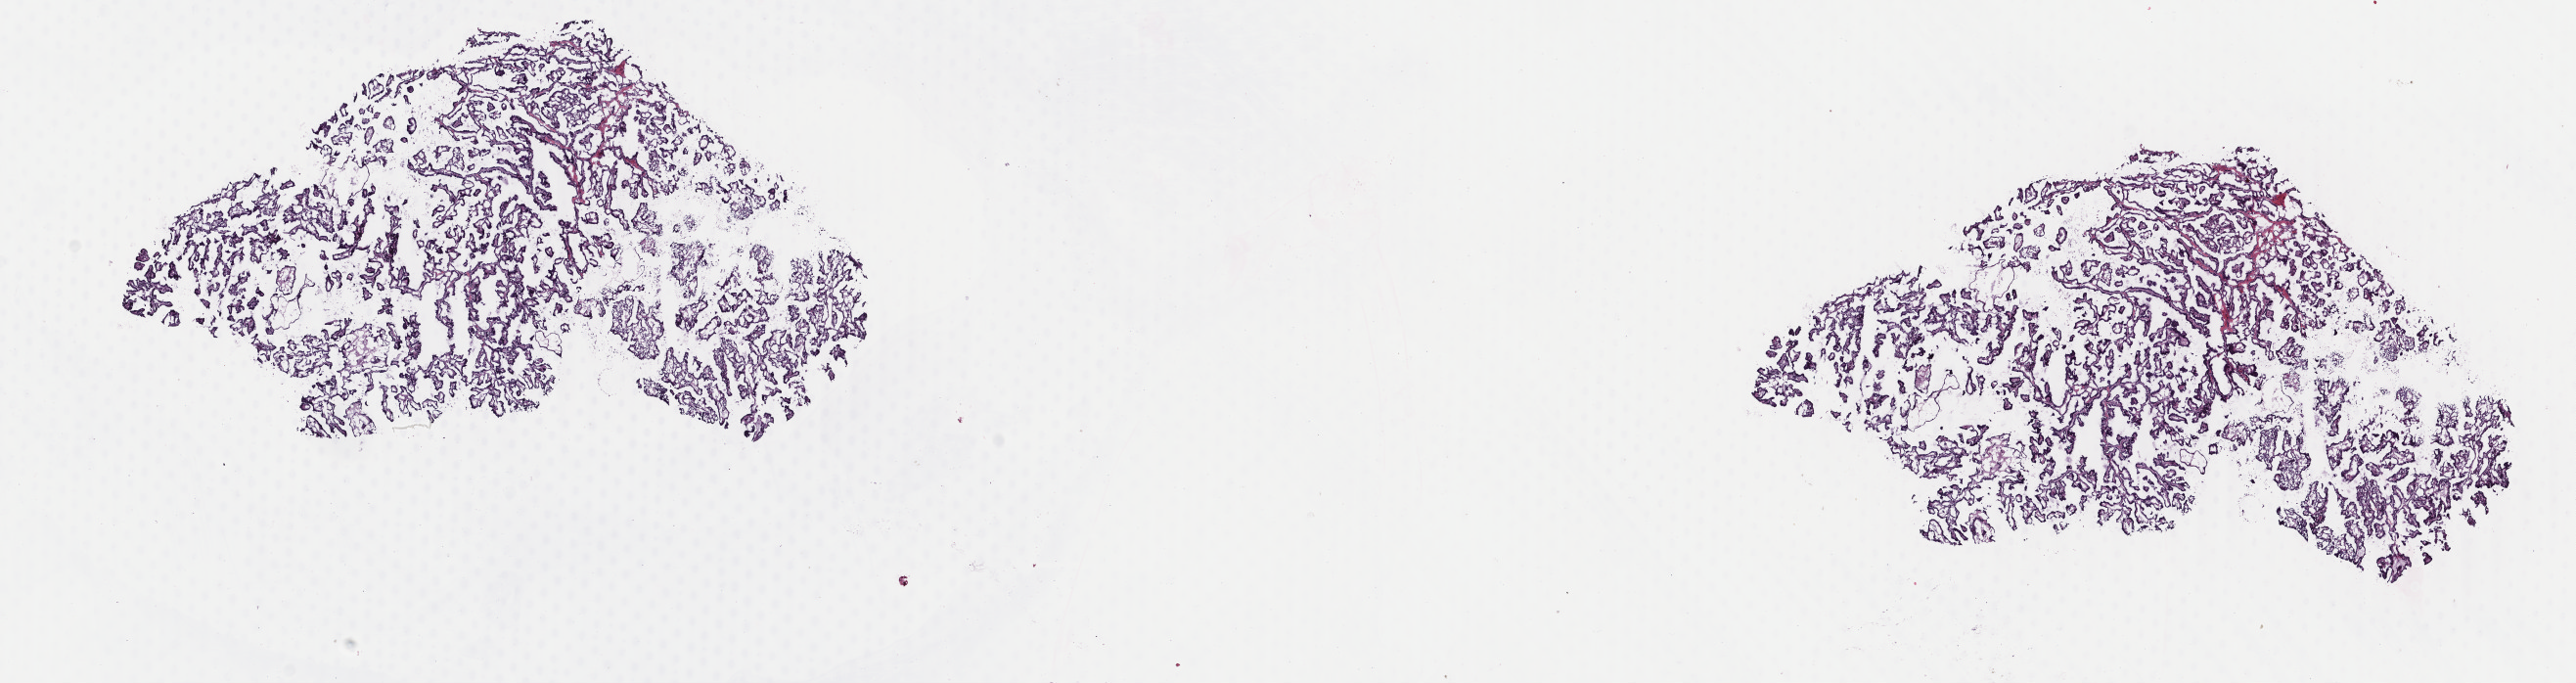
Whole-slide histology image, H&E-stained, low-resolution overview of the scanned area, about 20.9 x 5.6 mm (slide scanned at 40x), frozen section from the top of the tissue portion, thyroid, primary tumour sample. Female, age 37 years at initial diagnosis. Composition of this section per pathologist review: tumour cells 100%, tumour nuclei 95%, normal cells 0%, stromal cells 0%, necrosis 0%. Infiltration values recorded for this section: lymphocyte infiltration 0%, monocyte infiltration 0%, neutrophil infiltration 0%.
- histologic diagnosis: Papillary adenocarcinoma, NOS (thyroid gland)
- TNM: T2 N0 M0
- AJCC pathologic stage: I (7th edition)
- laterality: right